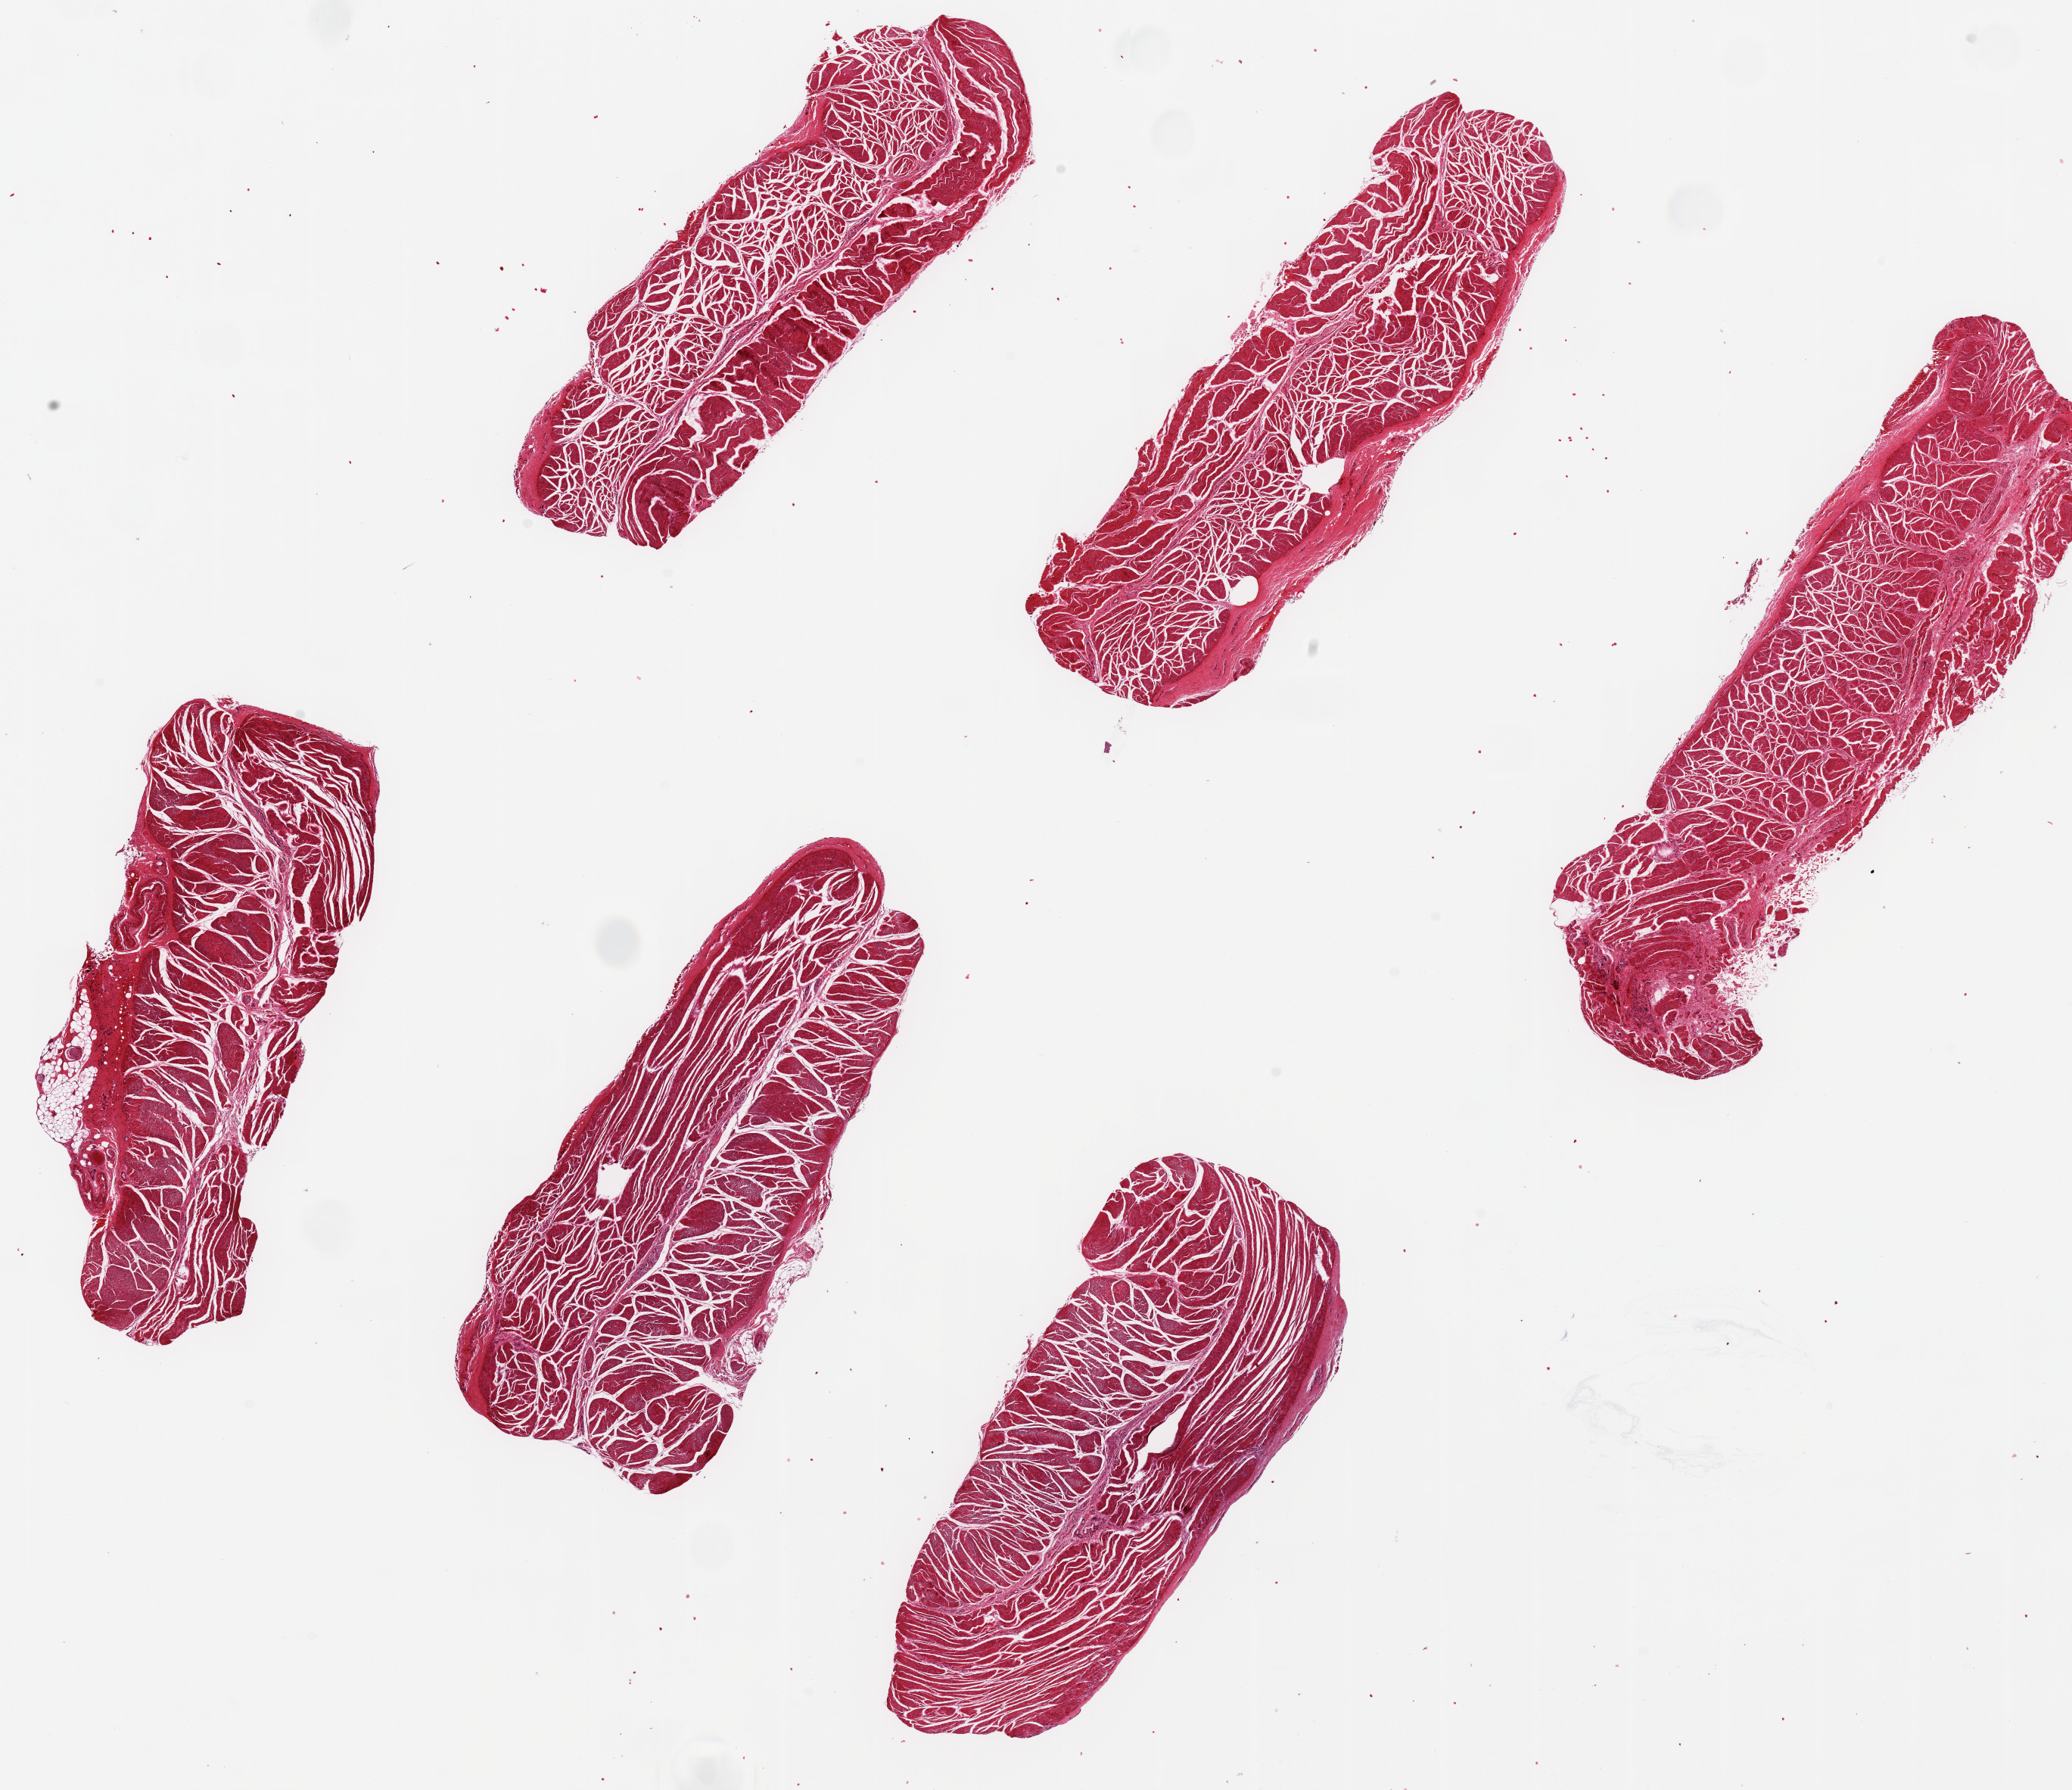
Whole-slide image, hematoxylin and eosin (H&E) stain — whole scanned area (about 21.7 x 18.7 mm, acquisition: 20x scan) shown as a low-resolution overview, PAXgene-fixed paraffin-embedded (PFPE) section, target tissue: esophageal muscle, donor tissue sample. Donor sex: female.
- pathologist's review note for this sample: 6 ~7x2.5mm pieces